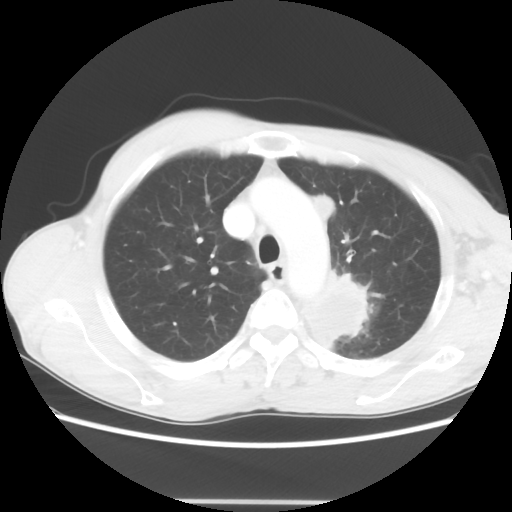
Chest CT, one axial slice; slice 49 of 62 in the series (ordered by position); reconstruction kernel STANDARD; lung window (W 1500 / L -600 HU); 5 mm slice thickness; 512 × 512 image matrix, field of view 360 × 360 mm. Male patient, age 61 years. Case-level facts recorded for this patient, not image findings: clinical TNM (as recorded): T3 N1 M1.
Annotated regions visible in this slice (rectangle marked by the reading radiologist):
- lung tumour (recorded histology: adenocarcinoma): bounding box (x1, y1, x2, y2) in pixels: (297, 270, 372, 352)
- lung tumour (recorded histology: adenocarcinoma): (309, 188, 331, 225)